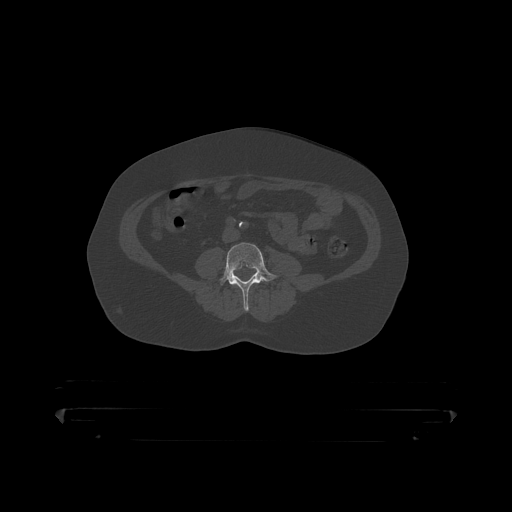
CT including the spine, one axial slice; slice 65 of 390 in the series (ordered by position); 120 kVp; bone window (W 1800 / L 400 HU); 1.25 mm slice thickness; 512 × 512 image matrix. Patient: male, 60 years. Case-level facts recorded for this patient, not image findings: primary cancer: prostate.
Structures marked on this image (semi-automatically segmented with operator editing):
- L3 vertebra: bounding box [x1, y1, x2, y2] px = [232, 284, 259, 289]
- L4 vertebra: [218, 243, 280, 311]